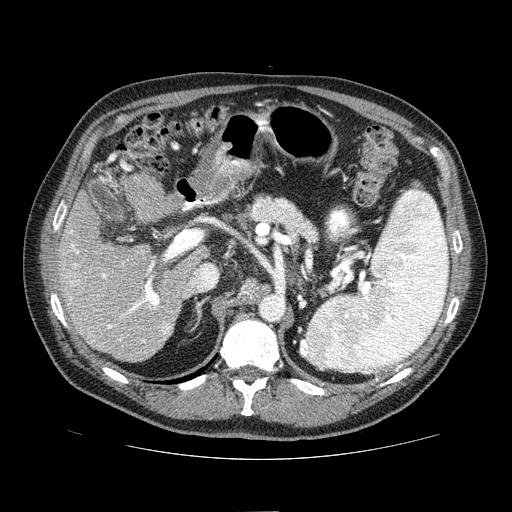
Contrast-enhanced abdominal CT (liver protocol), one axial slice. Slice 40 of 81 in the series (ordered by position). One of 2 acquisitions stored at this slice position. Soft-tissue window (W 400 / L 40 HU). 512 × 512 image matrix, field of view 400 × 400 mm. Case-level facts recorded for this patient, not image findings: diagnosis: hepatocellular carcinoma (patient treated with transarterial chemoembolisation; whether this scan precedes or follows treatment is not stated here); TNM stage (as recorded): Stage-IIIA; Child-Pugh class: A; tumour nodularity: multinodular.
Outlined on this slice (semi-automatic segmentation, software-assisted and operator-edited):
- liver parenchyma outside the tumour (the mass and vessels are separate outlines, so this box may not span the whole liver): bounding box (x1, y1, x2, y2) in pixels: (58, 182, 195, 362)
- liver vessels: (65, 230, 189, 343)